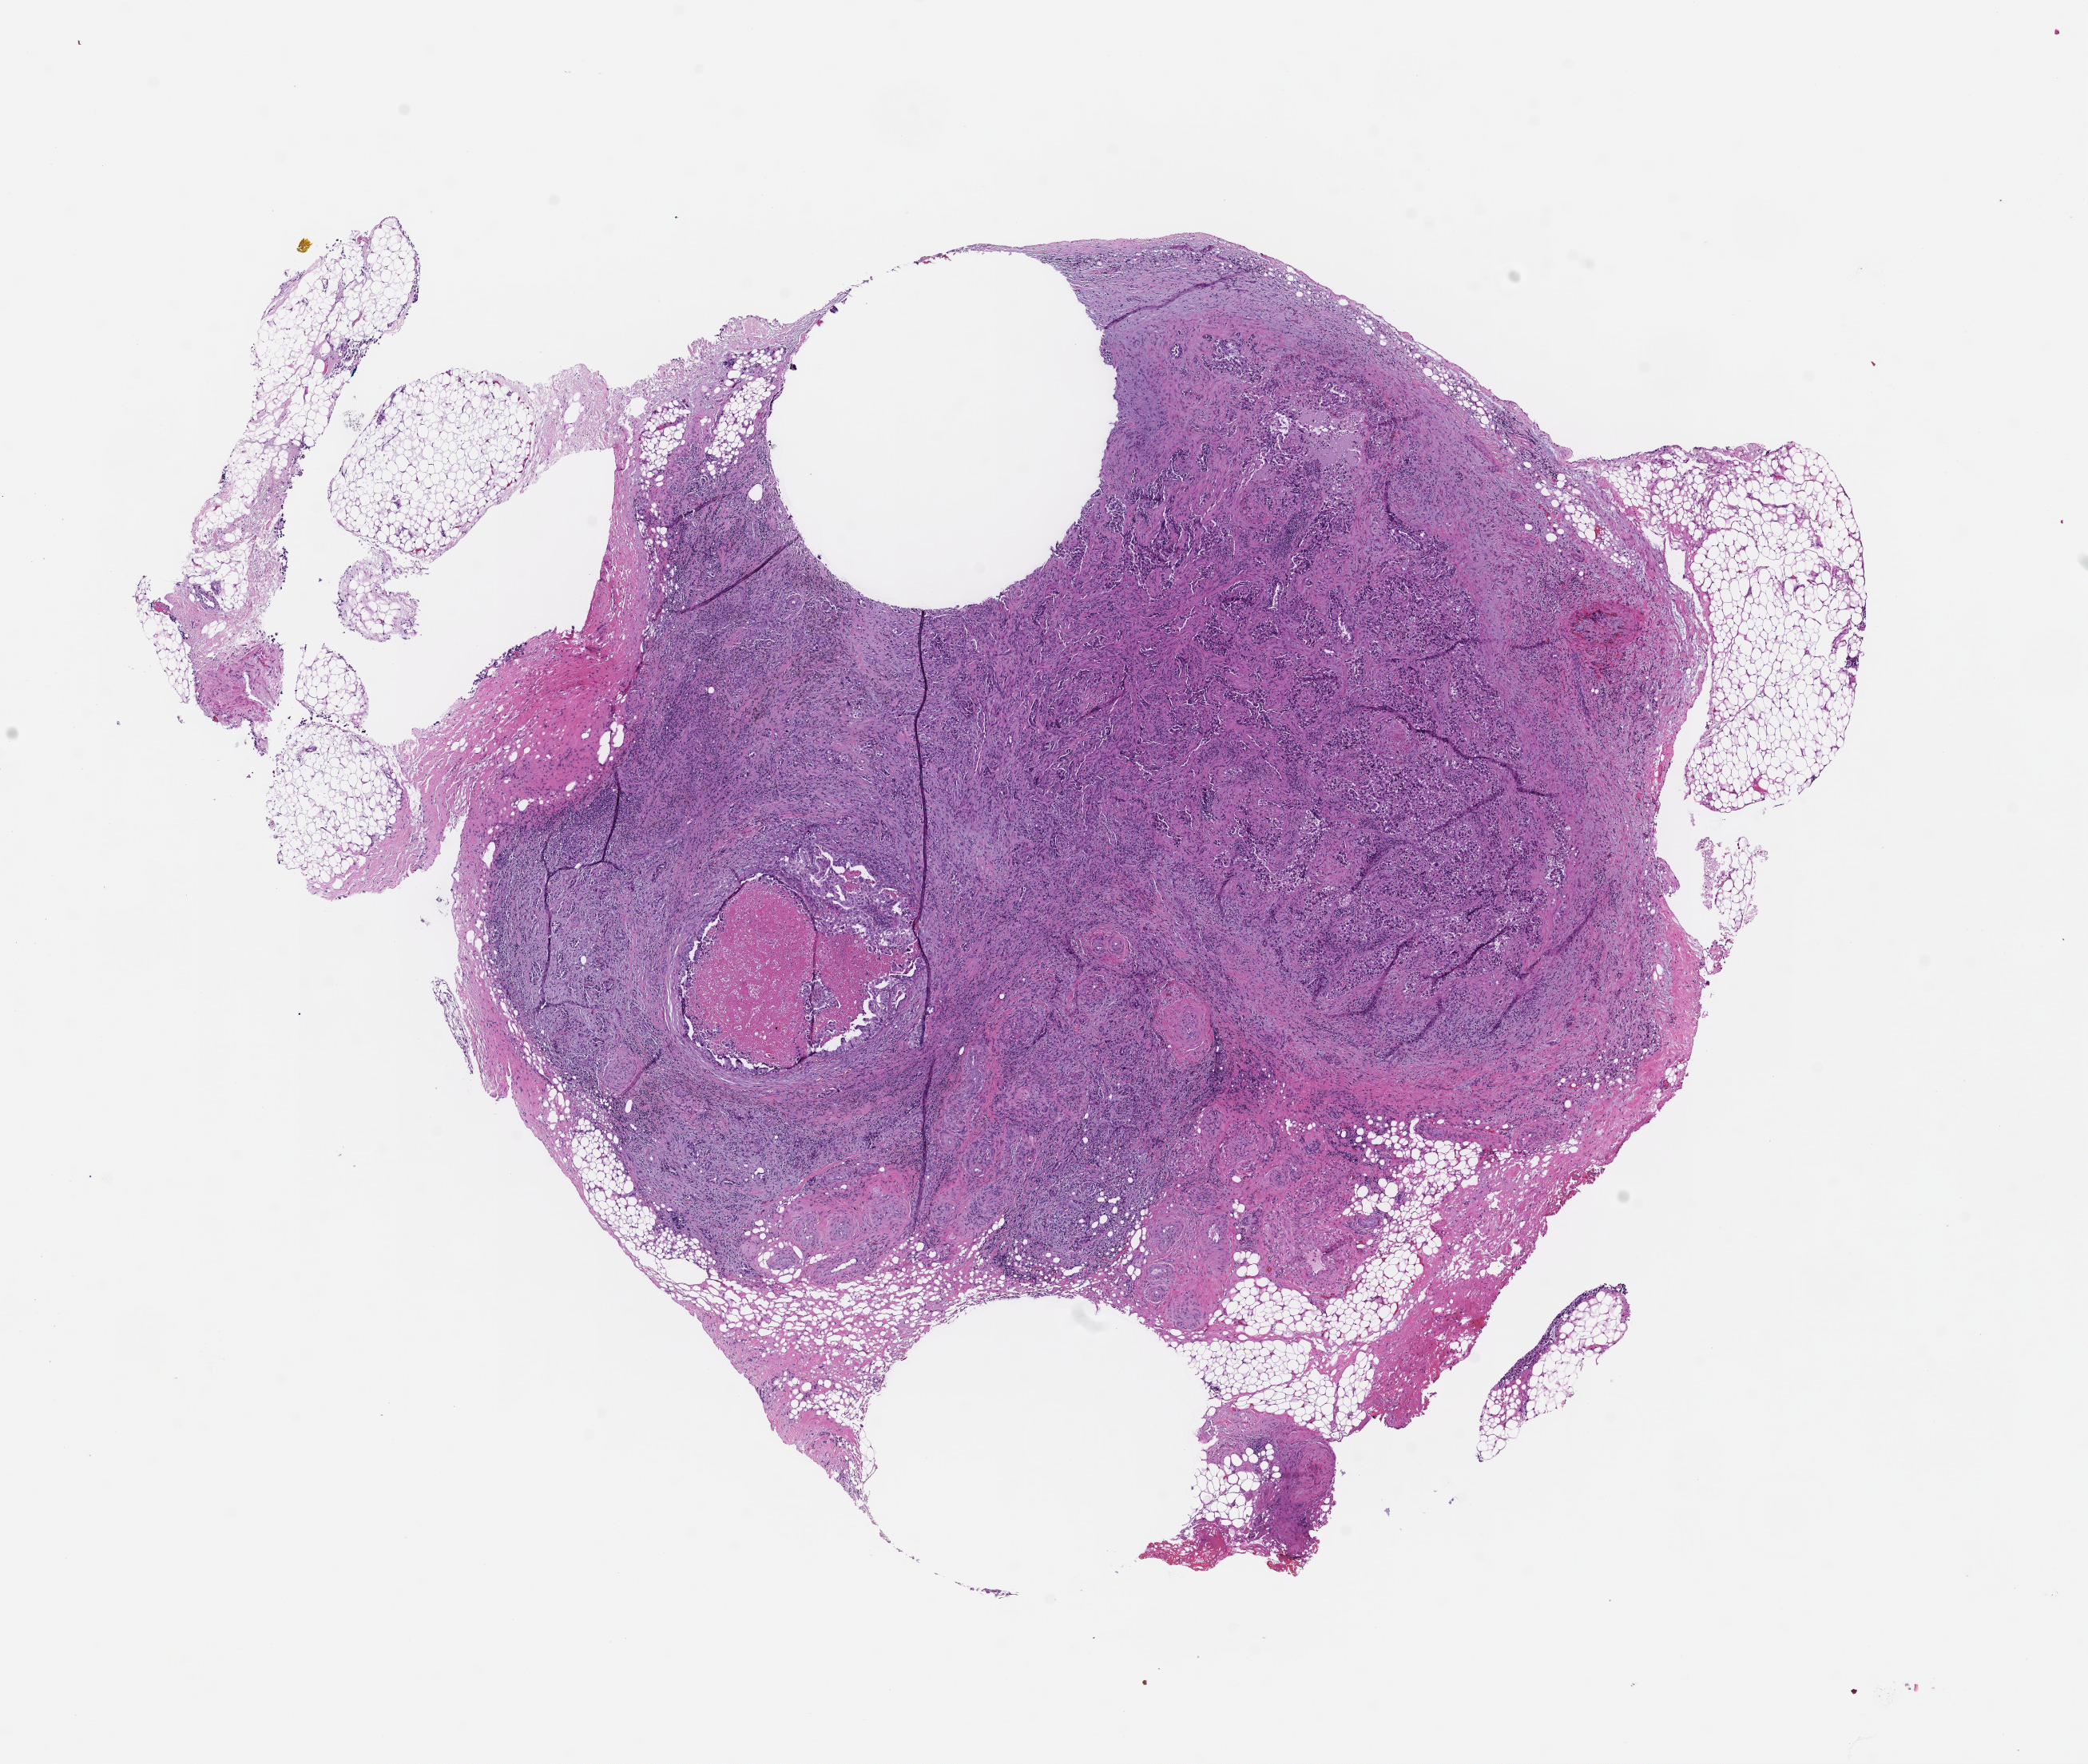
Whole-slide image, H&E stain — whole scanned area (about 10.6 x 8.9 mm) shown as a low-resolution overview; FFPE section. Patient: female.
This section: metastasis (sampled organ not recorded). Patient diagnosis (primary): Non-Small Cell Lung Carcinoma.